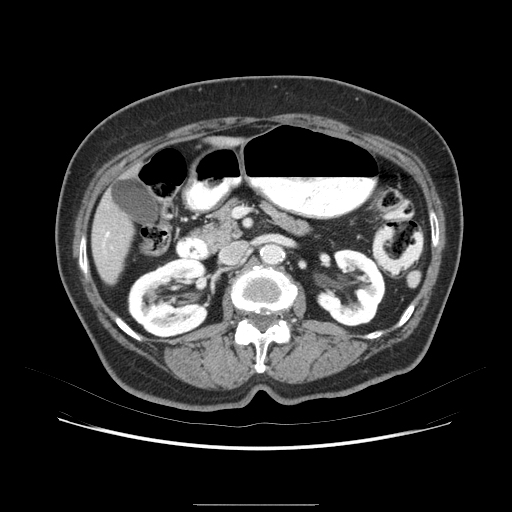
Contrast-enhanced abdominal CT (liver protocol), one axial slice; position 27 of 79 along the scan axis; 120 kVp; soft-tissue window (W 400 / L 40 HU); 512 × 512 image matrix. From the clinical record (not read from this slice): diagnosis: hepatocellular carcinoma (patient treated with transarterial chemoembolisation; whether this scan precedes or follows treatment is not stated here); TNM stage (as recorded): Stage-I; Child-Pugh class: A; tumour differentiation: poorly differentiated.
Outlined on this slice (semi-automatic segmentation, software-assisted and operator-edited):
- liver parenchyma outside the tumour (the mass and vessels are separate outlines, so this box may not span the whole liver): bounding box <90,132,256,300> (left, top, right, bottom; pixels)
- liver vessels: <119,219,146,245>